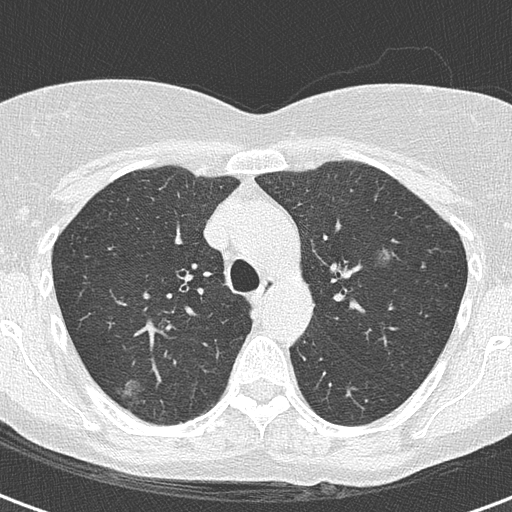
Low-dose screening chest CT, axial slice; second annual screen; lung window (W 1500 / L -600 HU); 2 mm slice thickness; 512 × 512 image matrix, field of view 283 × 283 mm. Female, age 56 years at enrolment. Current smoker at enrolment.
Expert reader's lesion annotation, bounding box [x1, y1, x2, y2] px = [89, 368, 154, 421]. Screening reader's record for this exam (one nodule recorded; not confirmed to be the boxed lesion): non-calcified nodule or mass ≥4 mm, right upper lobe, 18 × 18 mm, mixed attenuation, pre-existing on the prior screen: yes.